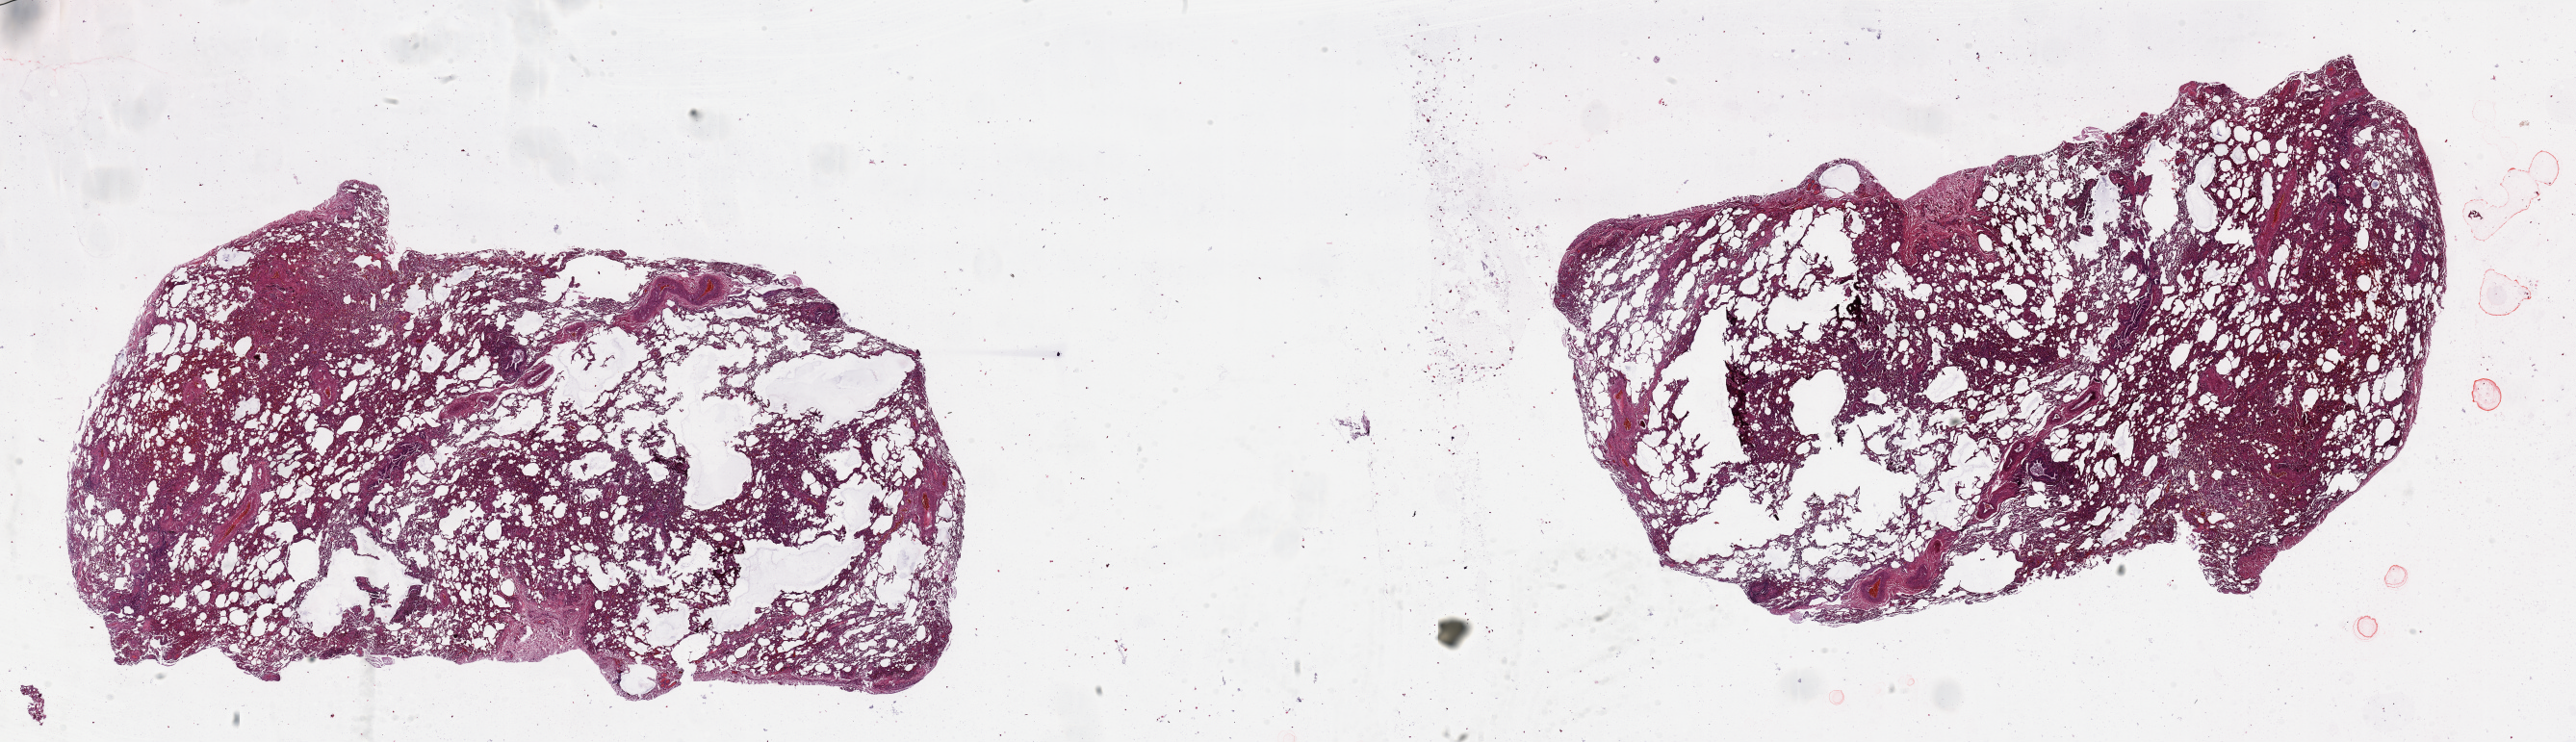
H&E-stained whole-slide image — whole scanned area (about 42.3 x 12.2 mm, from a 20x scan) shown as a low-resolution overview. Normal (non-tumour) tissue sample, sampled site: lung. Patient: male, age 57 years.
This section: normal (non-tumour) tissue from the same patient. Patient diagnosis: Squamous cell carcinoma, NOS.